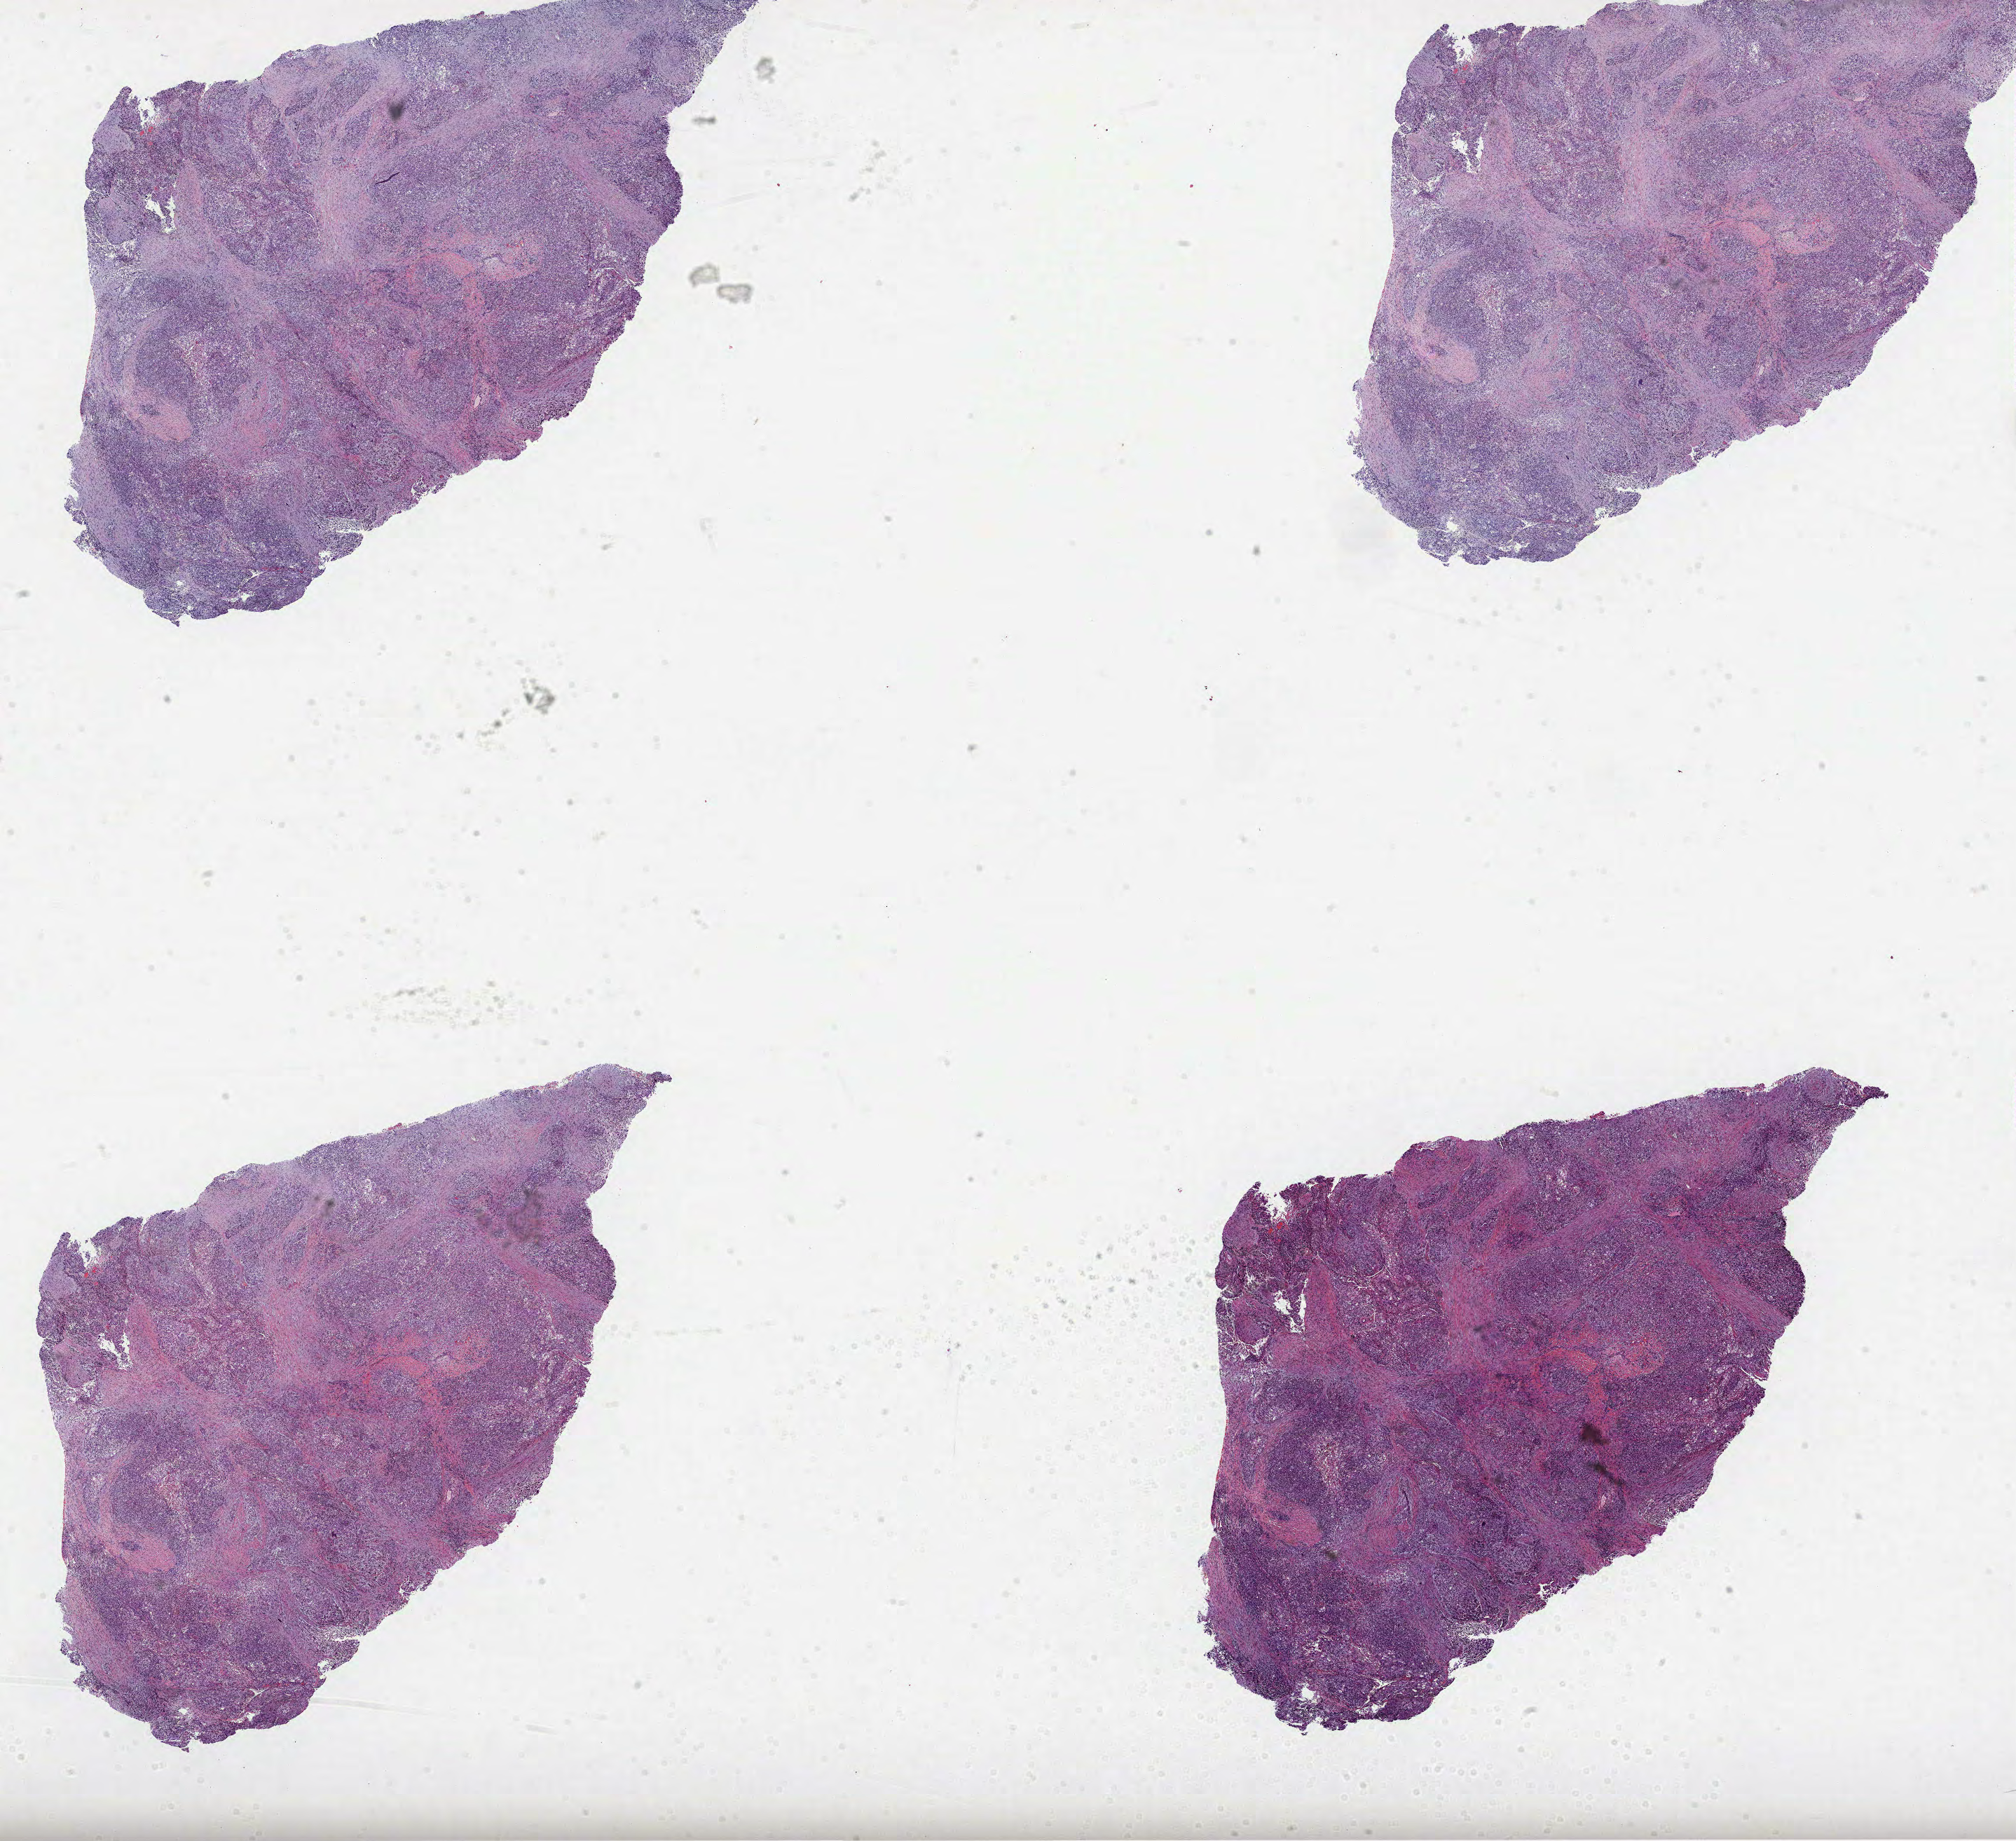
H&E whole-slide image, shown as a low-resolution overview of the whole scanned area (about 23.2 x 21.2 mm, from a 40x scan), formalin-fixed paraffin-embedded (FFPE) diagnostic section, sample: primary tumour, lung. Patient: male, age at initial diagnosis 71 years.
AJCC pathologic stage: IB (7th edition). Diagnosis: Squamous cell carcinoma, NOS (upper lobe, lung). Laterality: right.